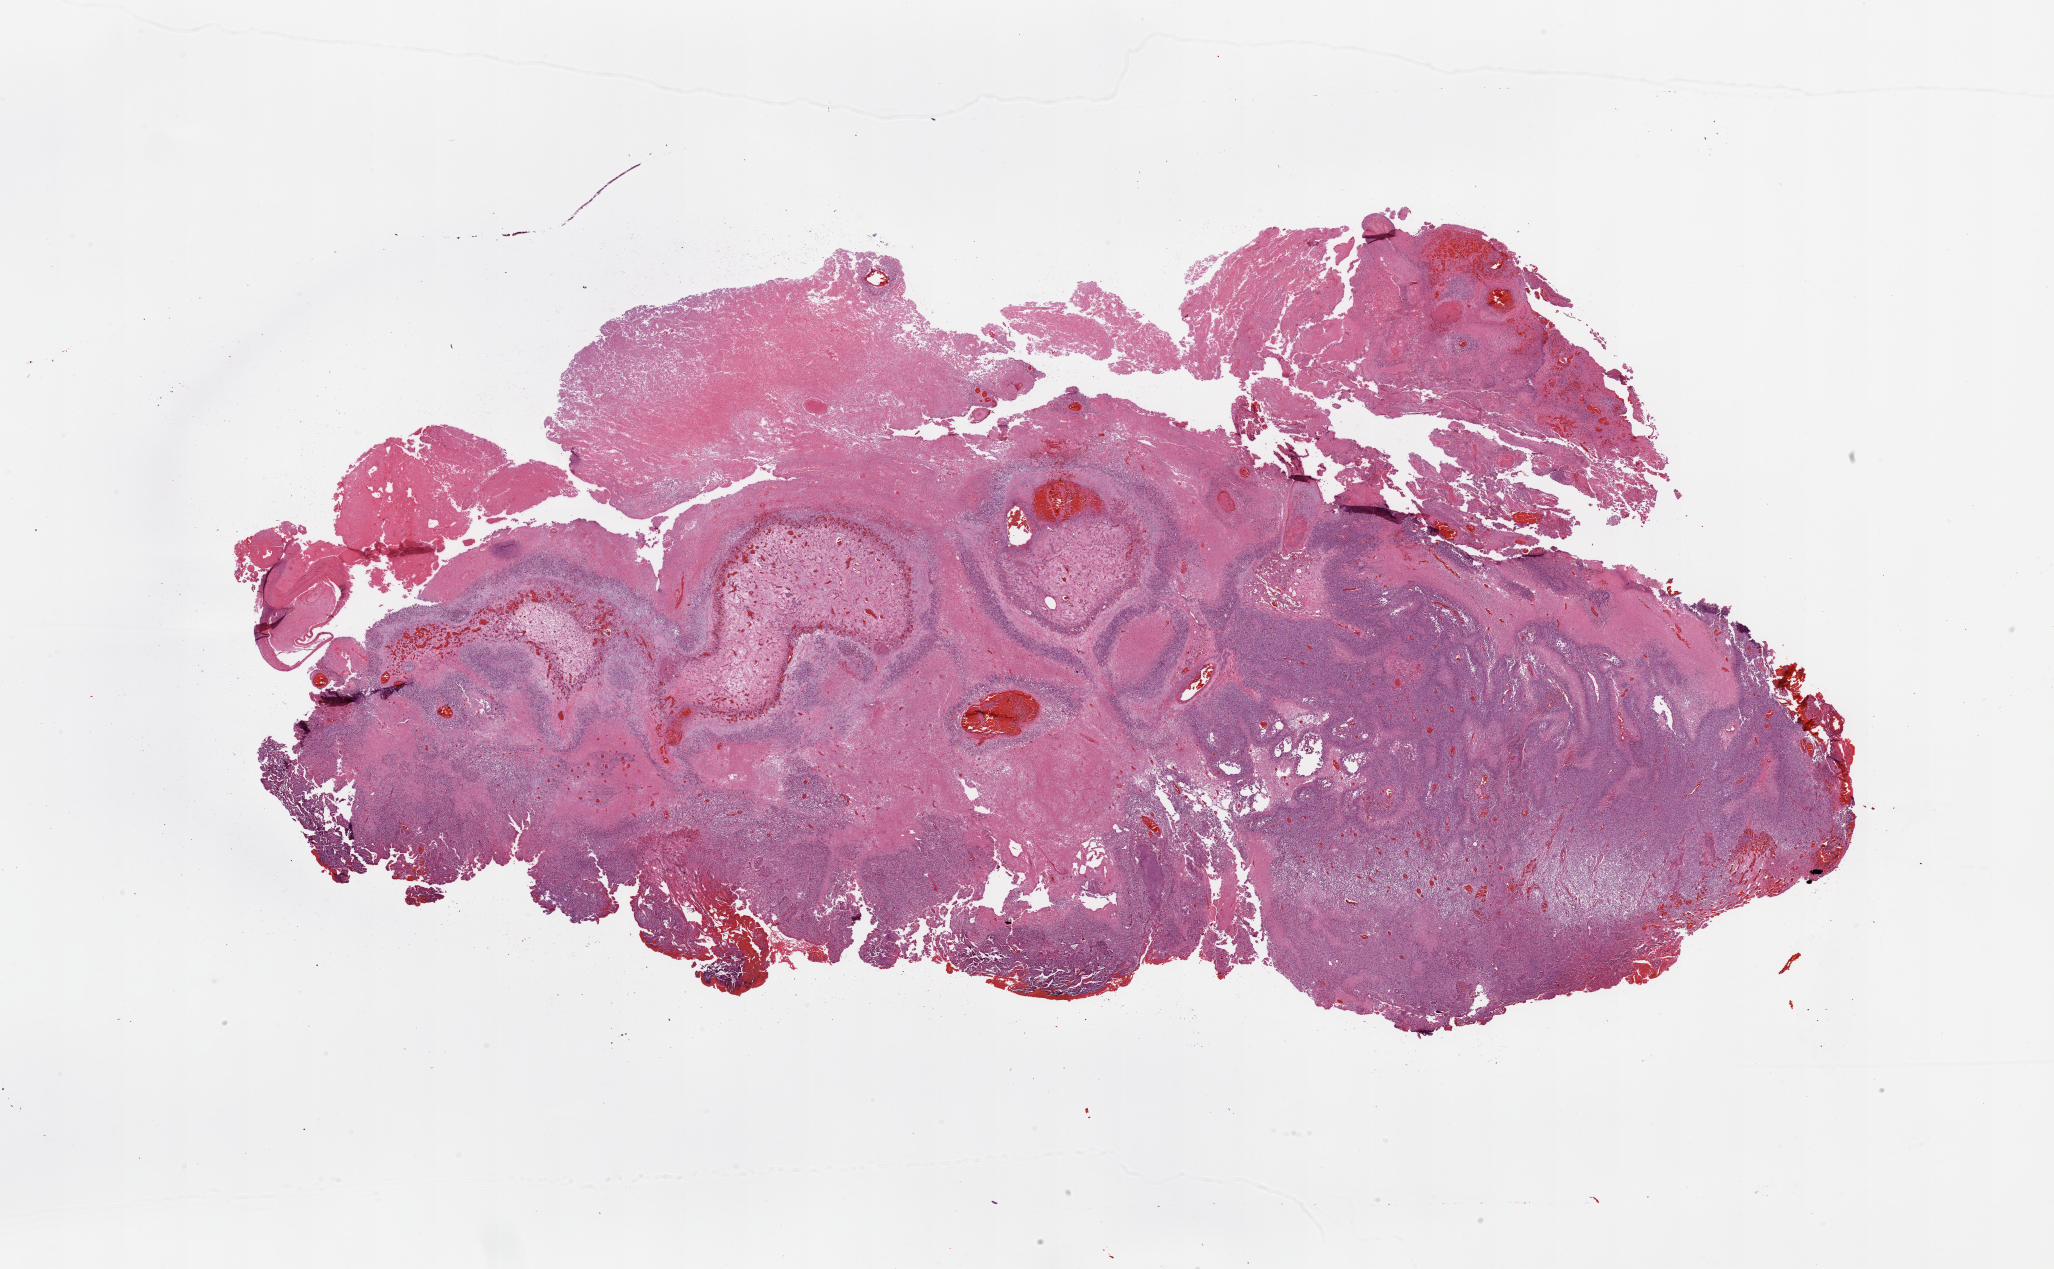
Hematoxylin and eosin (H&E) stained whole-slide image, low-resolution overview of the scanned area, about 32.5 x 20.1 mm (slide scanned at 20x); tumour tissue sample, brain. Patient: male, age 62 years.
Primary tumour site (as recorded): frontal lobe. Patient diagnosis (cohort enrolment): glioblastoma multiforme (brain).